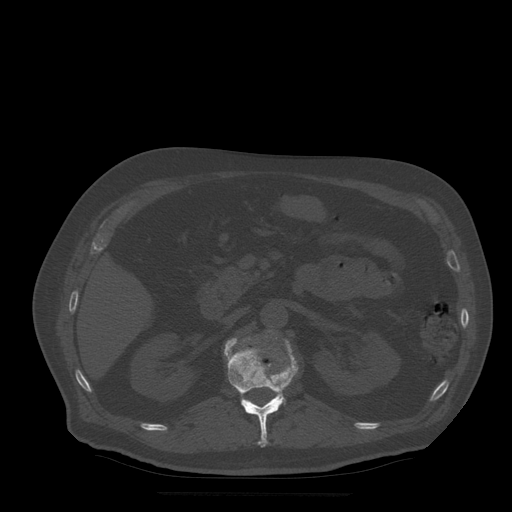
CT including the spine, one axial slice; slice 191 of 522 in the series (ordered by position); bone window (W 1800 / L 400 HU); 1.25 mm slice thickness; 512 × 512 image matrix. Patient age 72 years. From the clinical record (not read from this slice): primary cancer: prostate.
Annotated regions visible in this slice (semi-automatically segmented with operator editing):
- L1 vertebra: box from (x=224, y=338) to (x=299, y=447) px
- L2 vertebra: (x=269, y=331)–(x=274, y=402)